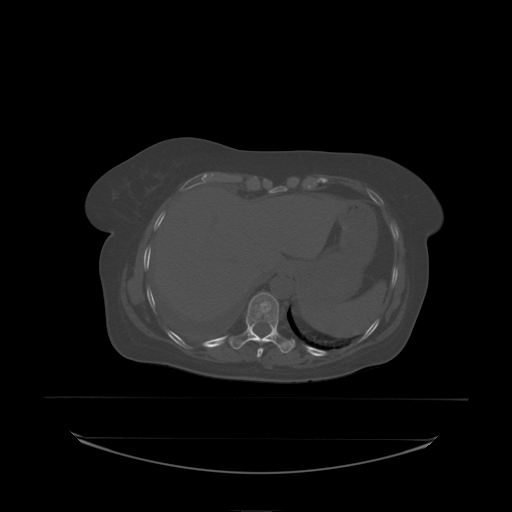
CT including the spine, one axial slice. Slice 115 of 242 in the series (ordered by position). Bone window (W 1800 / L 400 HU). 2.5 mm slice thickness. 512 × 512 image matrix, field of view 500 × 500 mm. Patient: female, 53 years. From the clinical record (not read from this slice): primary cancer: lung.
Outlined on this slice (semi-automatic segmentation, software-assisted and operator-edited):
- T10 vertebra: box from (x=241, y=293) to (x=279, y=338) px